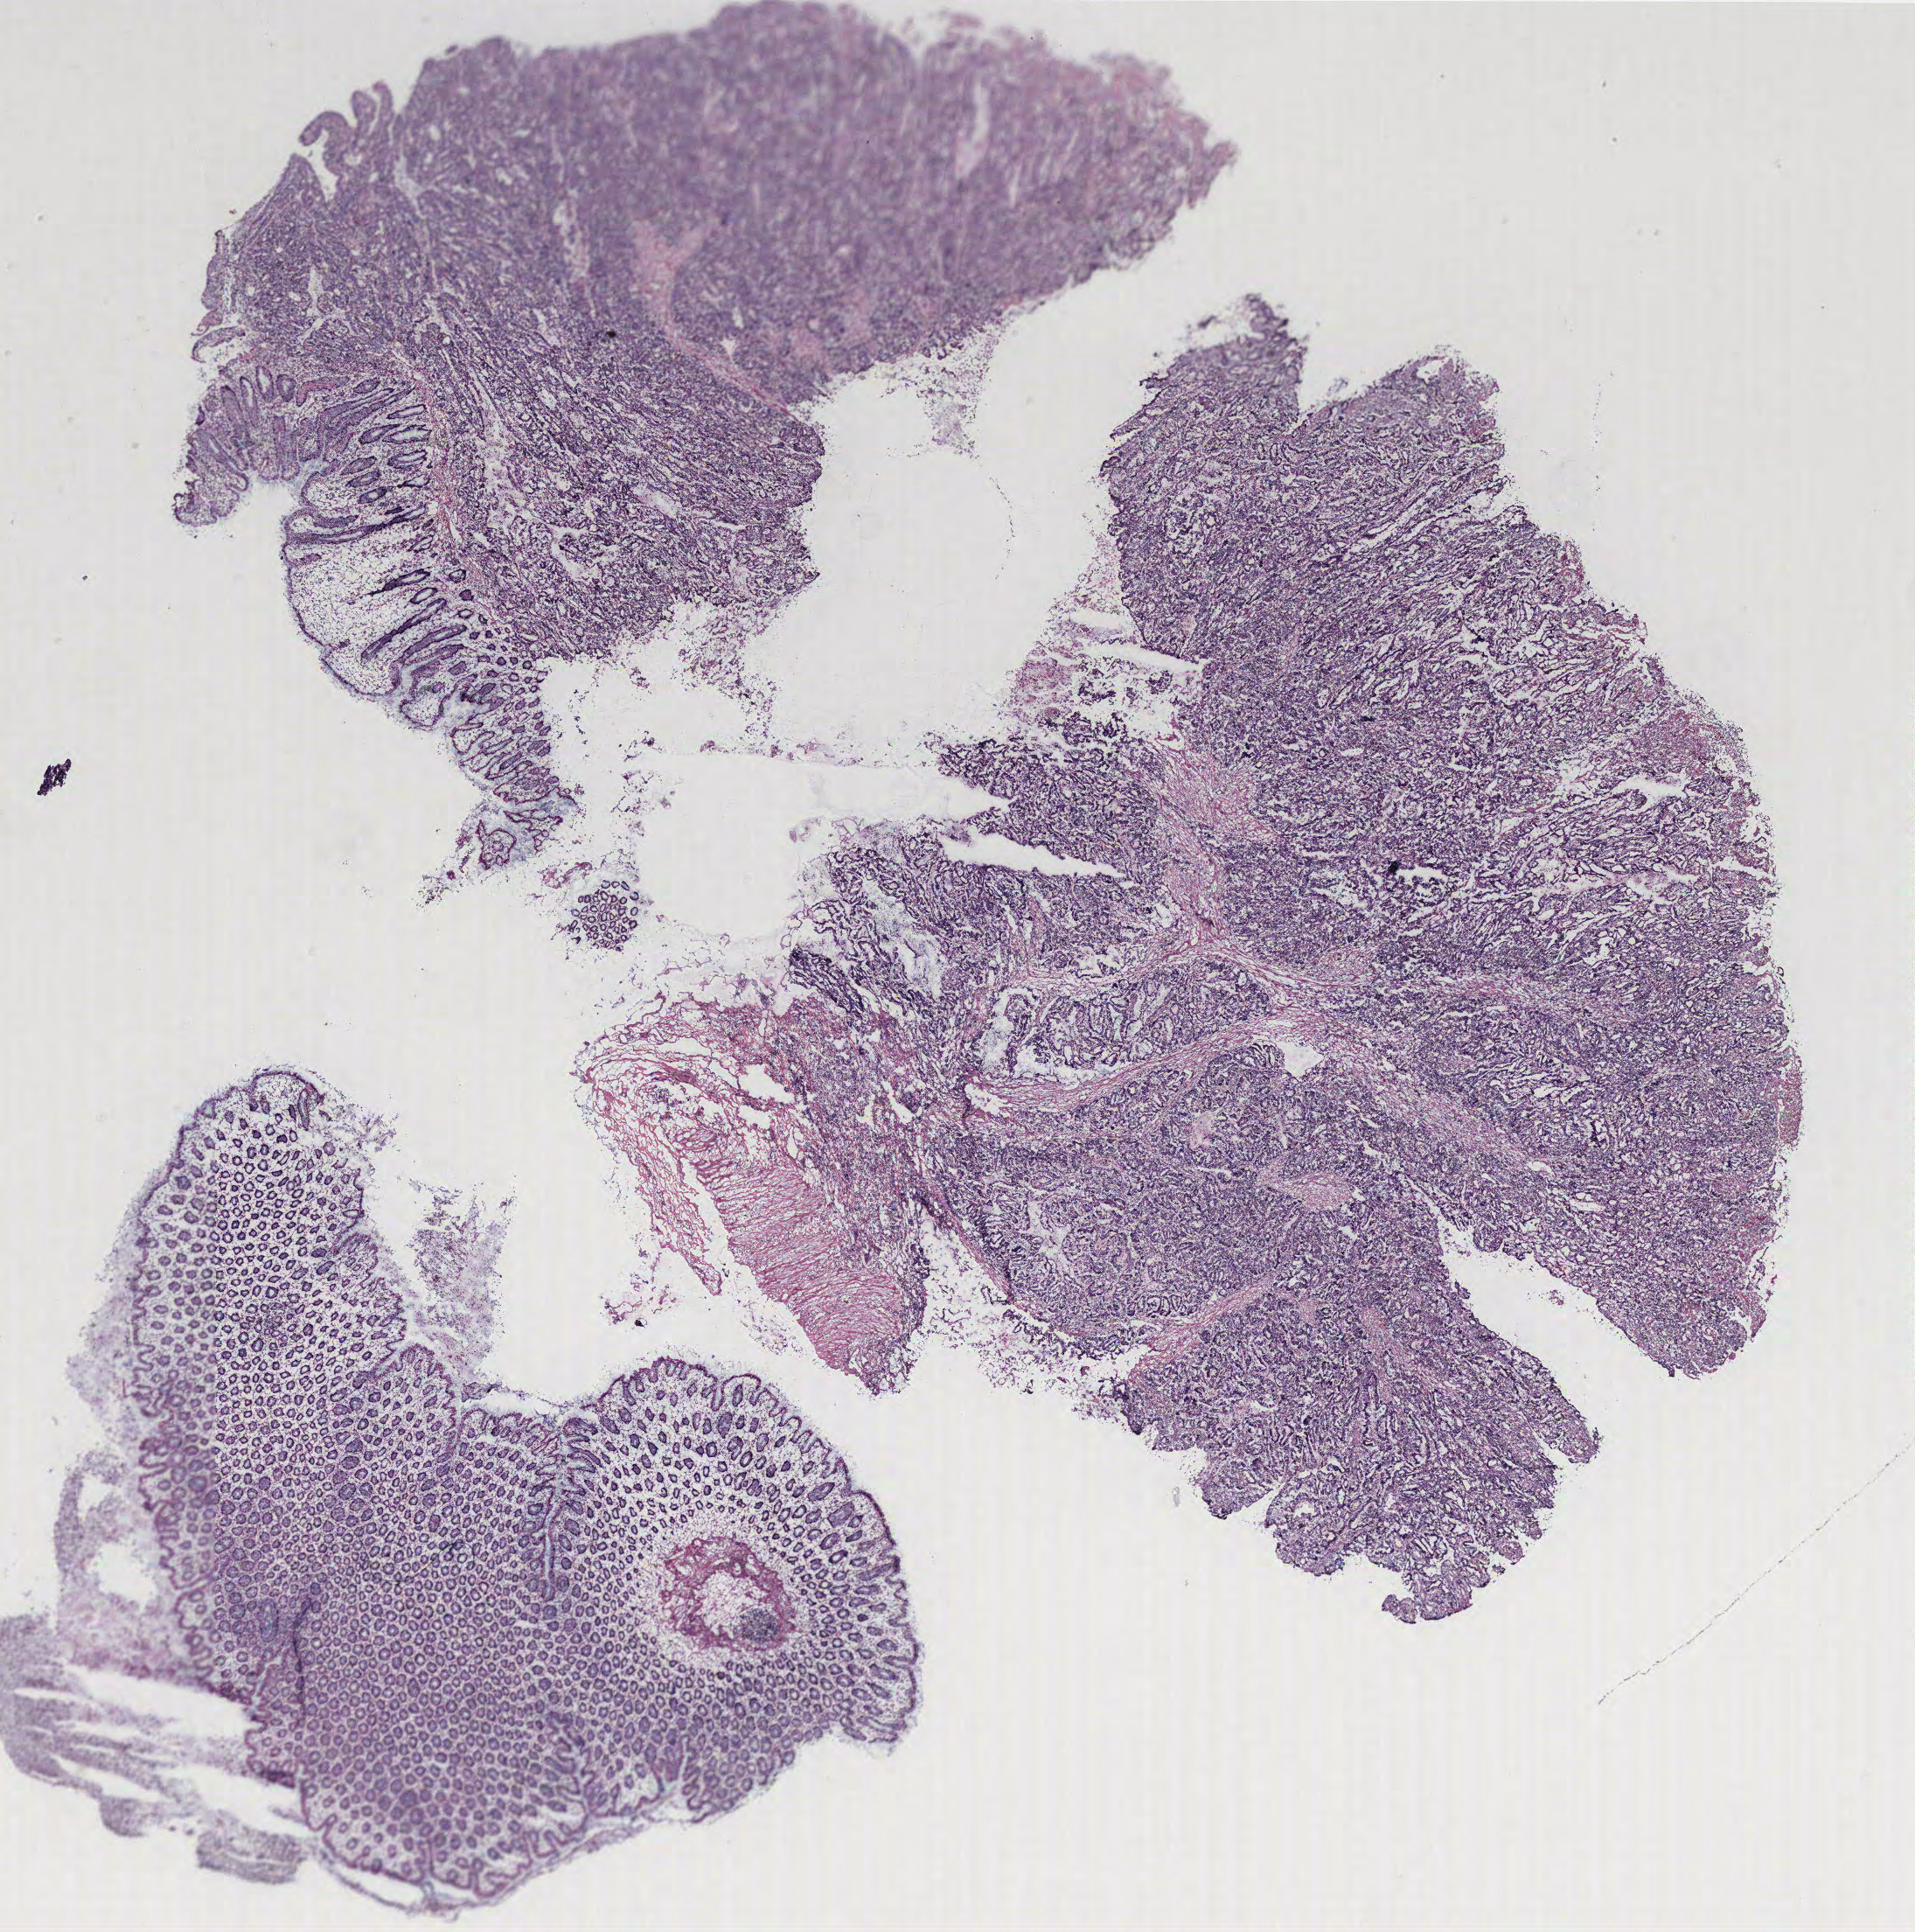
Whole-slide histology image, H&E — whole scanned area (about 17.5 x 17.7 mm) shown as a low-resolution overview, normal (non-tumour) tissue sample, colon. Patient: female, age 53 years.
This section: normal (non-tumour) tissue from the same patient. Patient diagnosis: Adenocarcinoma, NOS.